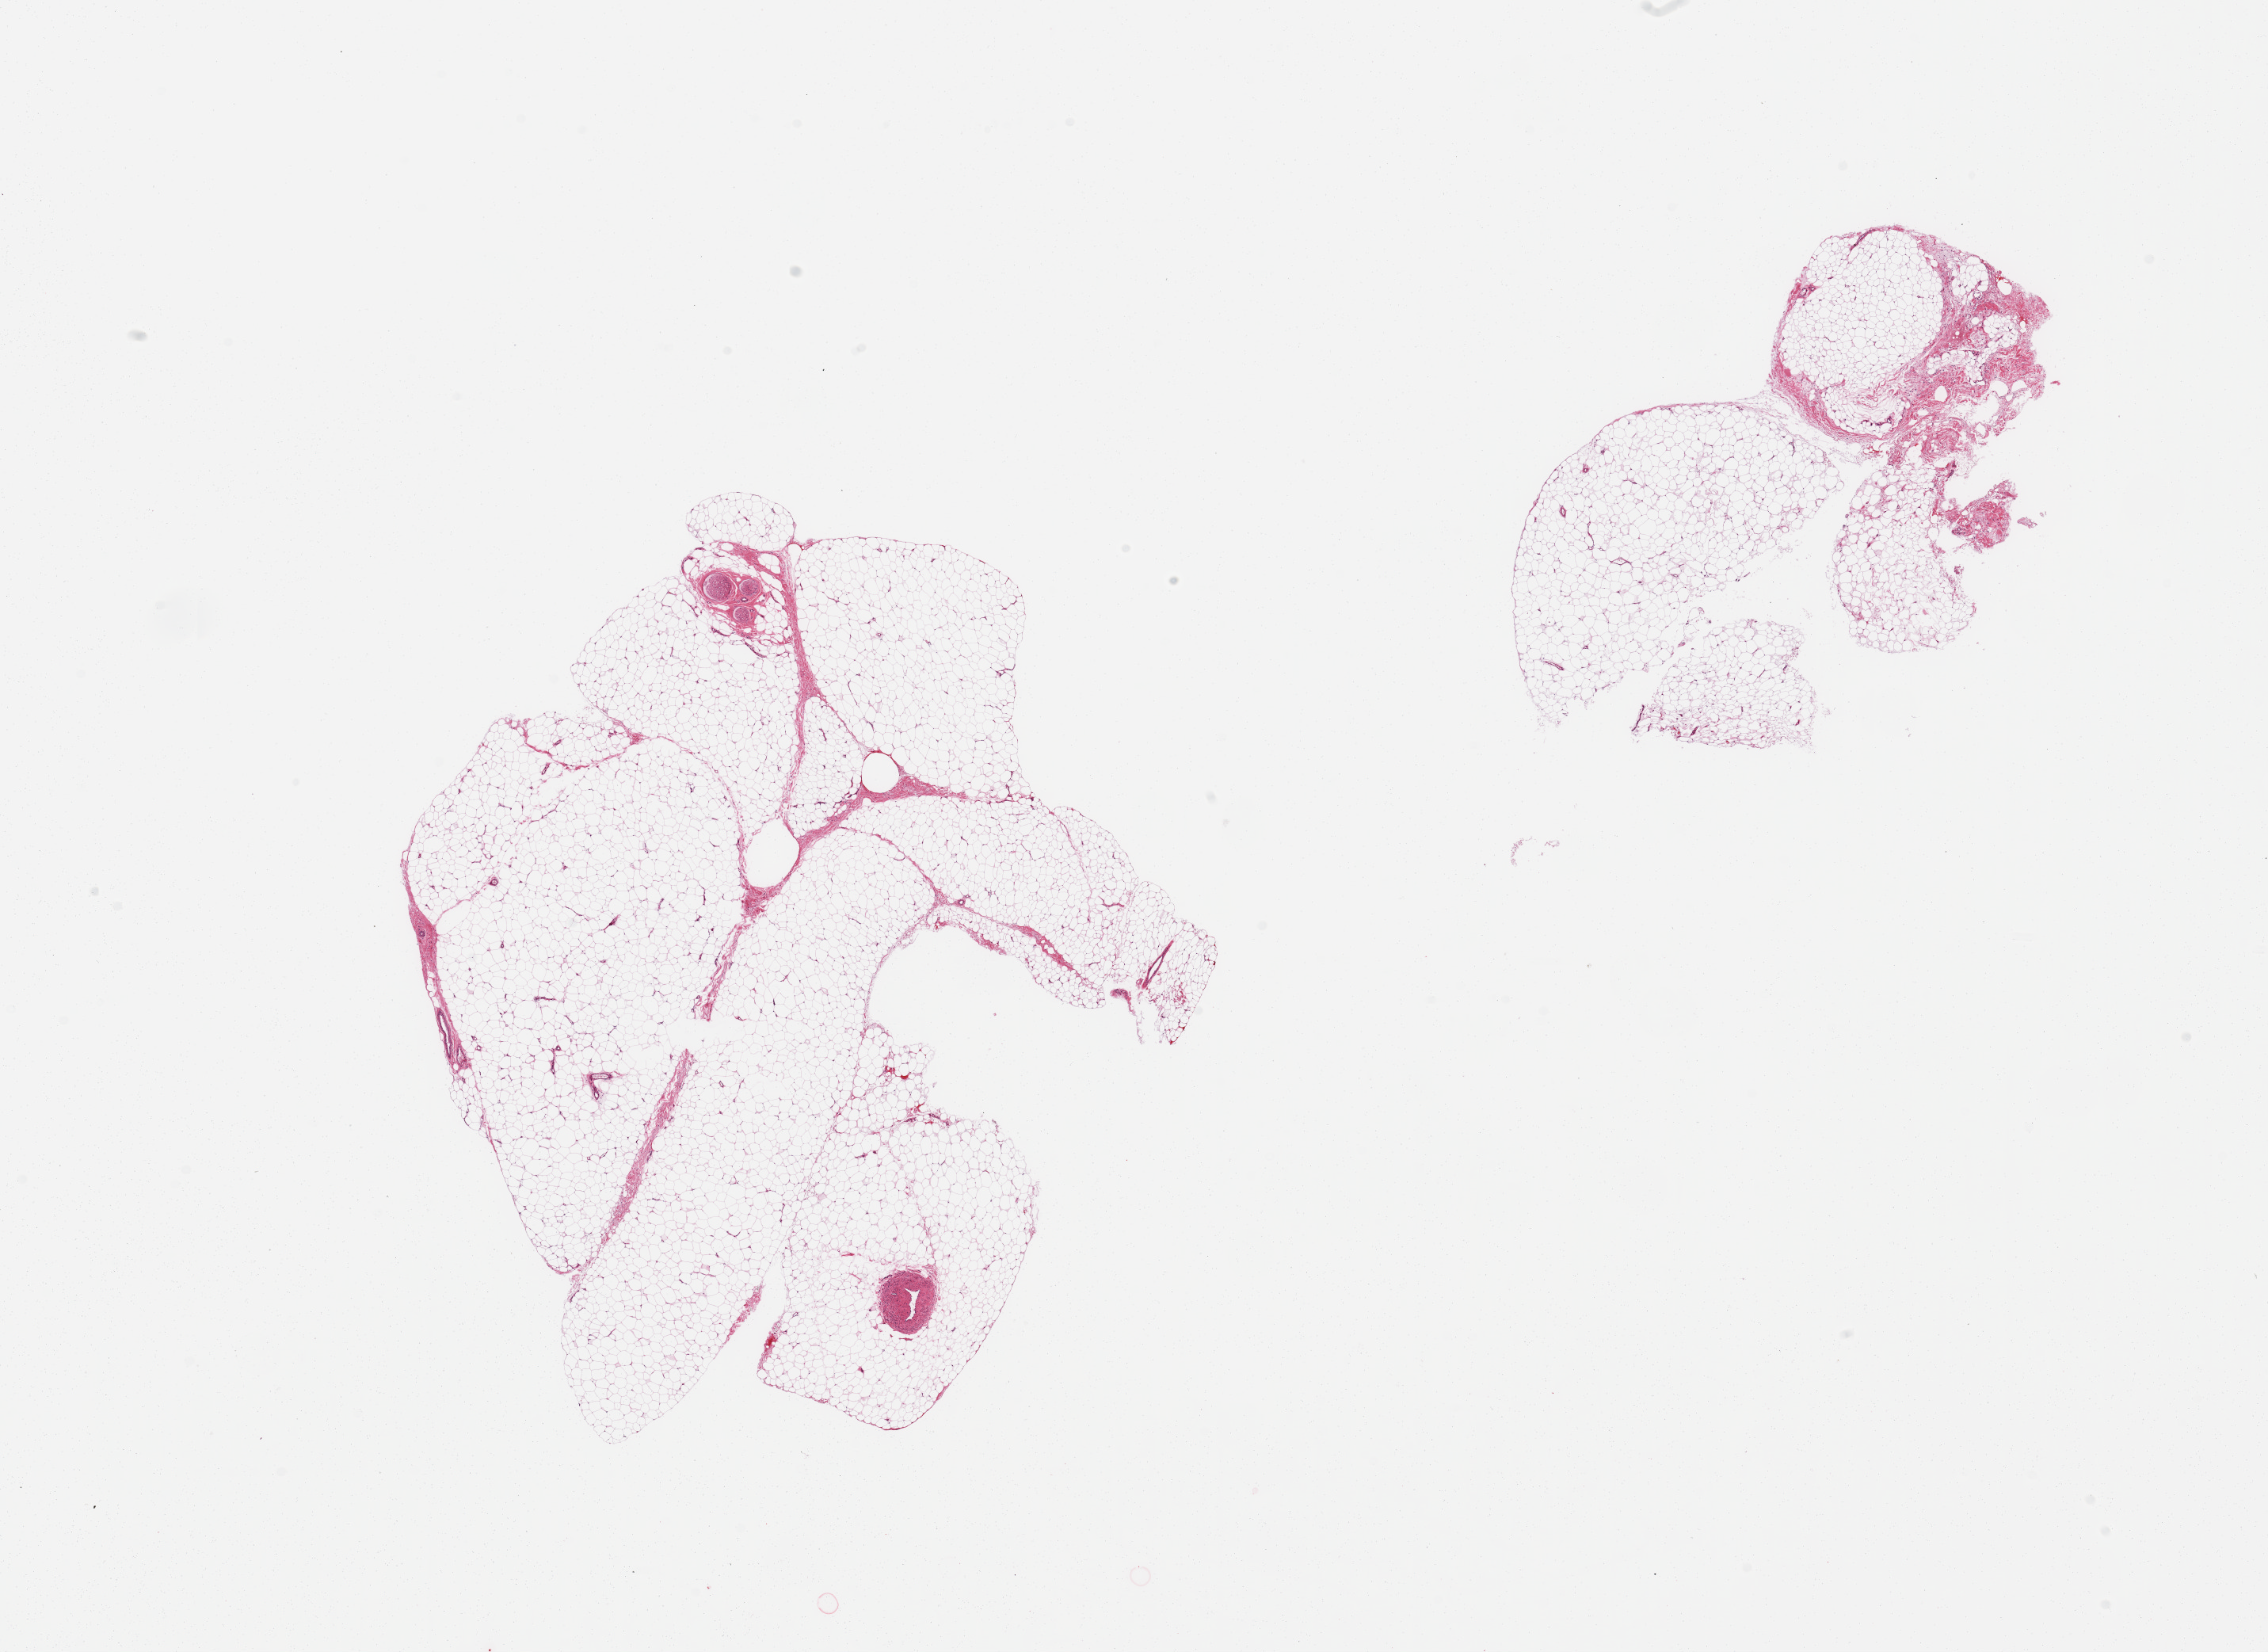
Whole-slide image, hematoxylin and eosin (H&E) stain, brightfield — shown as a low-resolution overview of the whole scanned area (about 22.6 x 16.5 mm, slide scanned at 20x); PAXgene-fixed, paraffin-embedded tissue; target tissue: adipose tissue; tissue donor sample.
Reviewer comment on this tissue sample: 2 pieces; 5% fibrovascular content.